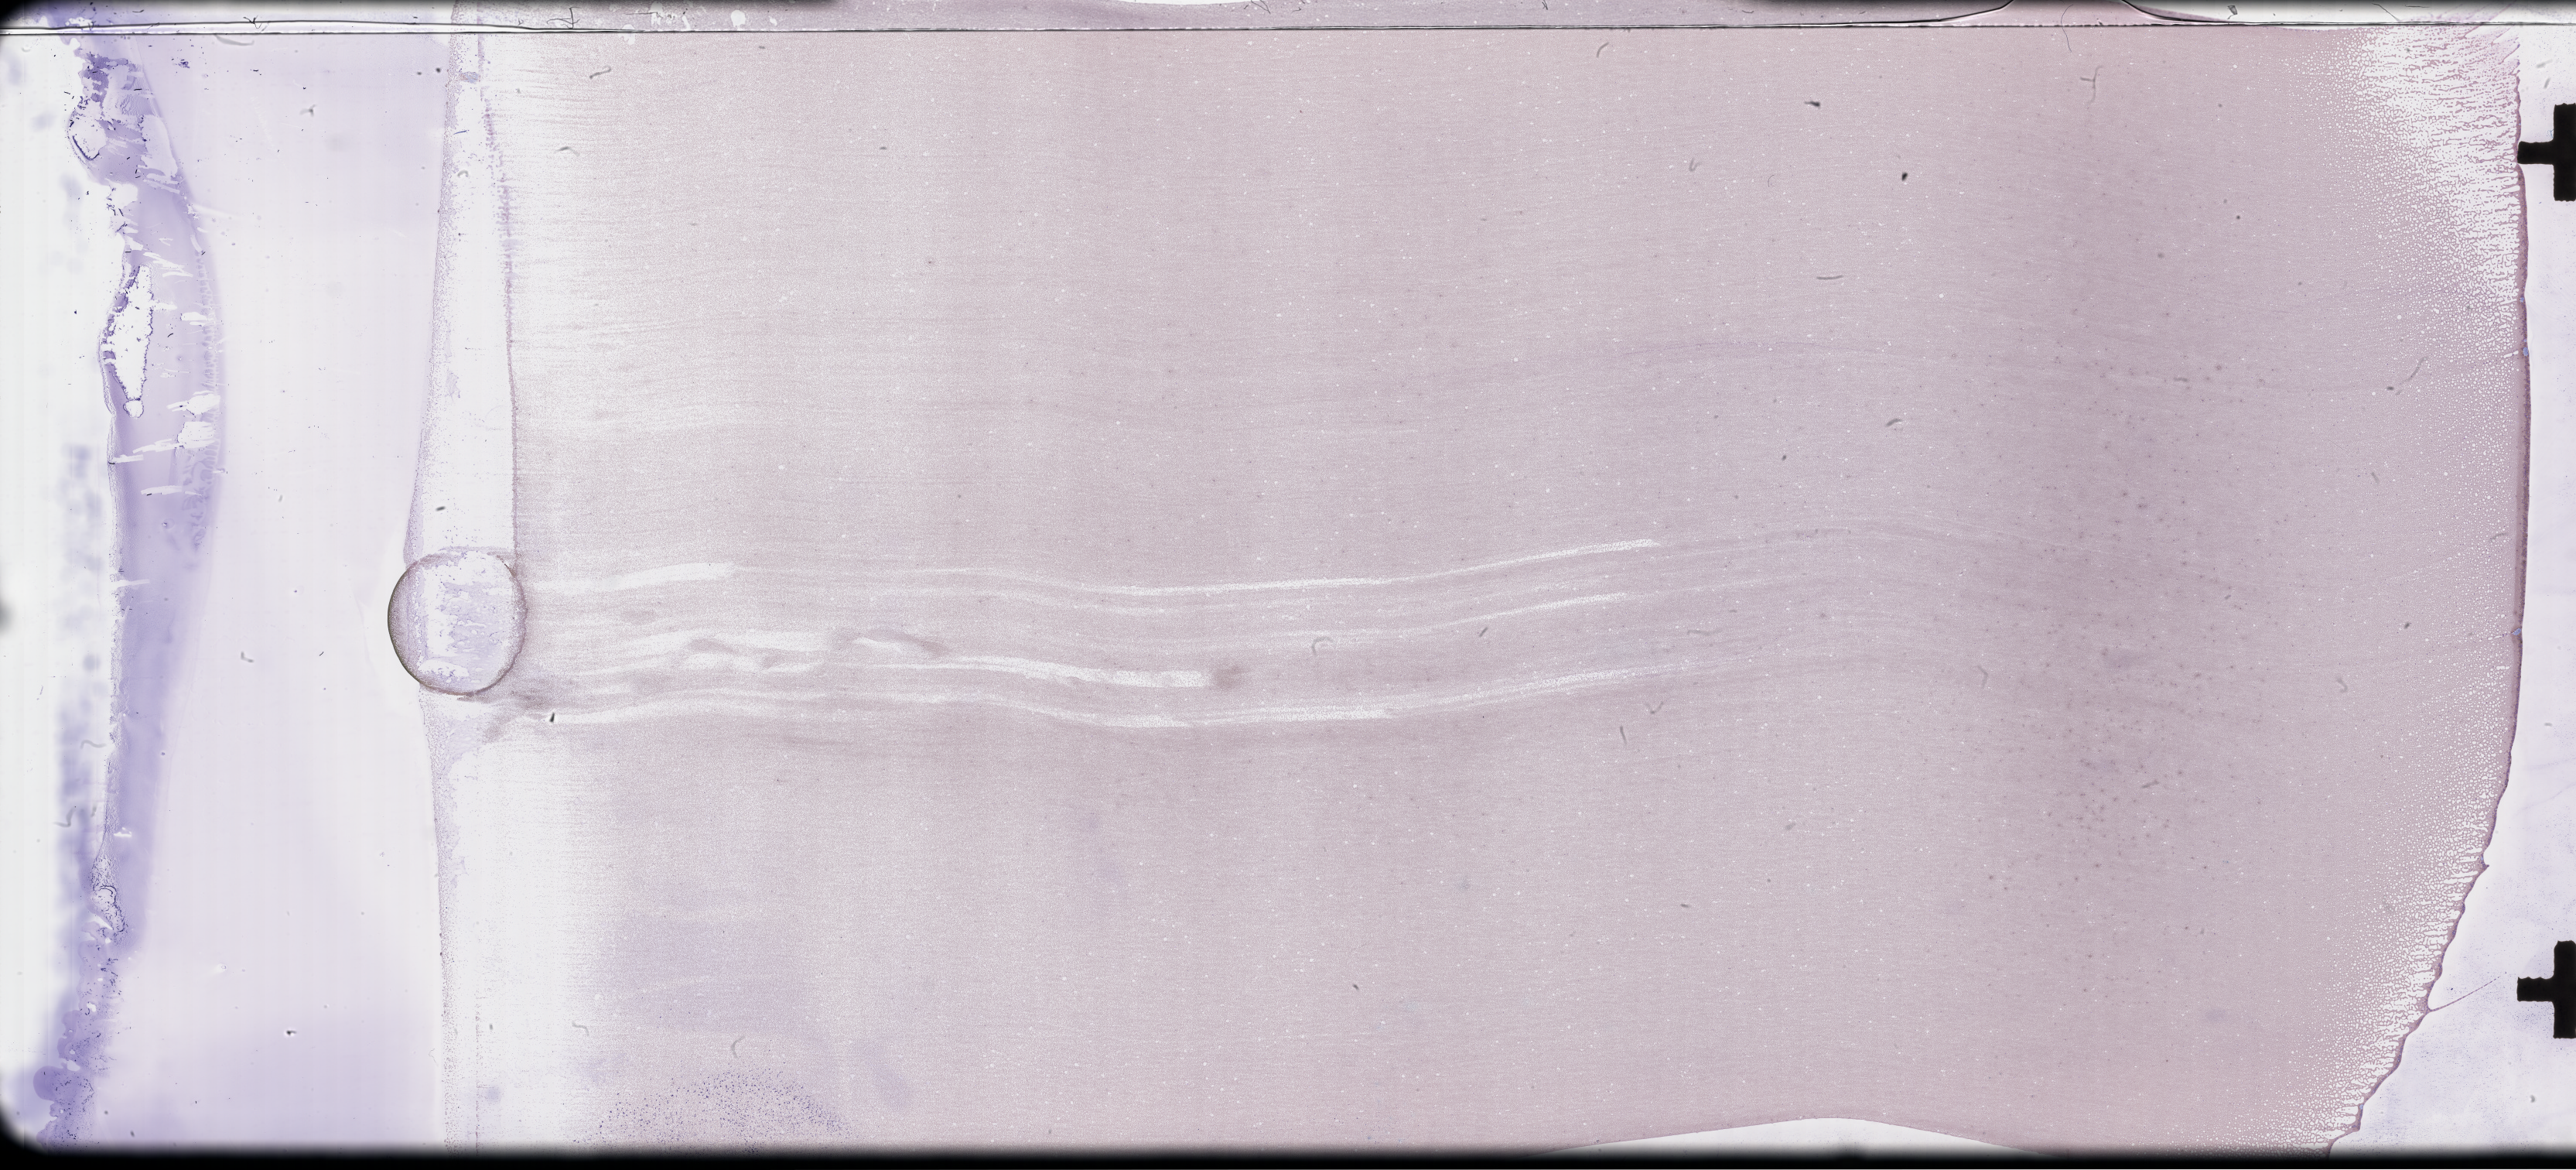
Whole-slide image of a whole blood smear, Wright-Giemsa stain, shown as a low-resolution overview of the whole scanned area (about 53.8 x 24.4 mm). Female patient.
Patient diagnosis: Plasma Cell Myeloma.